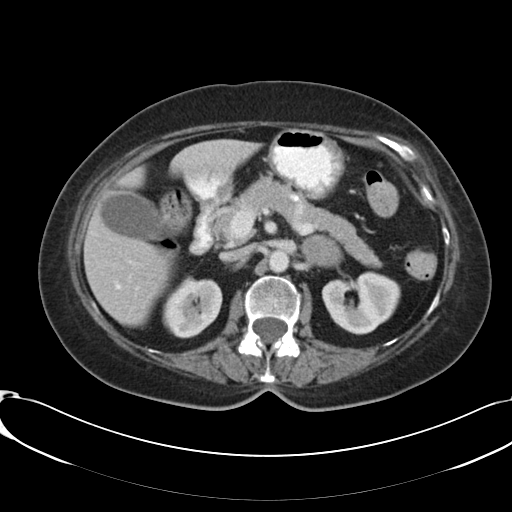
Contrast-enhanced abdominal CT, one axial slice. Position 66 of 91 along the scan axis. Intravenous contrast given. Soft-tissue window (W 400 / L 40 HU). 5 mm slice thickness. 512 × 512 image matrix, field of view 366 × 366 mm. Female patient, age 73 years. Case-level facts recorded for this patient, not image findings: diagnosis: adrenocortical carcinoma; tumour side: left adrenal.
Outlined on this slice (semi-automatic segmentation, software-assisted and operator-edited):
- mass: bounding box (x1, y1, x2, y2) in pixels: (302, 236, 342, 266)